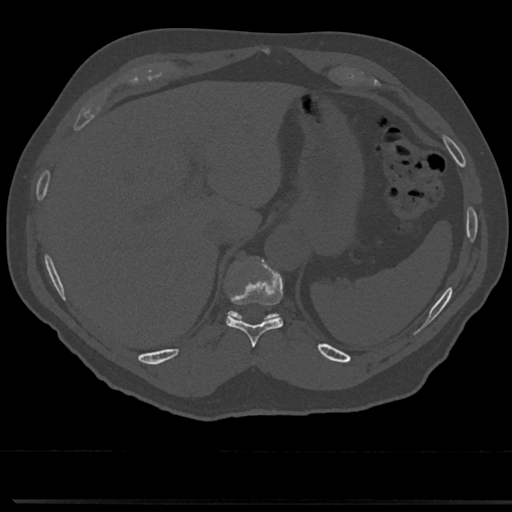
CT including the spine, one axial slice; position 244 of 817 along the scan axis; 120 kVp; bone window (W 1800 / L 400 HU); 0.5 mm slice thickness; 512 × 512 image matrix, field of view 355 × 355 mm. Patient: male, 61 years. Case-level facts recorded for this patient, not image findings: primary cancer: prostate.
Annotated regions visible in this slice (semi-automatic segmentation, software-assisted and operator-edited):
- T10 vertebra: bounding box <224,257,284,345> (left, top, right, bottom; pixels)
- T11 vertebra: <229,313,277,321>